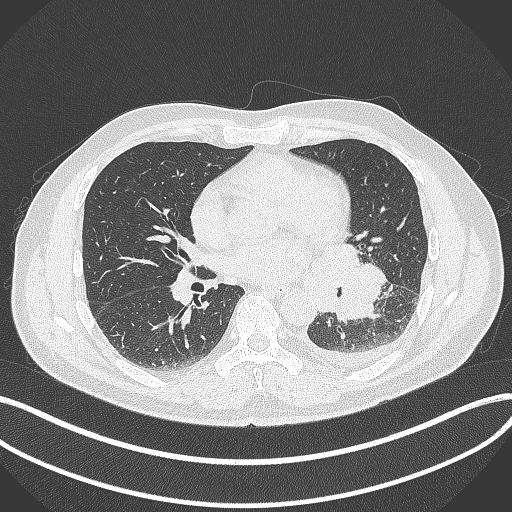
Chest CT, one axial slice; slice 171 of 342 in the series (ordered by position); reconstruction kernel B70f; 120 kVp; lung window (W 1500 / L -600 HU); 1 mm slice thickness; 512 × 512 image matrix, field of view 400 × 400 mm. Patient: male, 58 years. Case-level facts recorded for this patient, not image findings: clinical TNM (as recorded): T3 N1 M1b.
Structures marked on this image (bounding box drawn by a radiologist):
- lung tumour (recorded histology: small cell carcinoma): bounding box <312,236,385,322> (left, top, right, bottom; pixels)